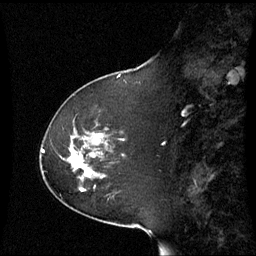
Breast MRI (dynamic contrast-enhanced), one sagittal slice; dynamic contrast-enhanced series, image 2 of 3 at this slice position (ordered by acquisition); 1.5 T; TE 4.2 ms, TR 8.9 ms; 2.4 mm slice thickness; 256 × 256 image matrix, field of view 230 × 230 mm. Female patient, age 51 years. From the clinical record (not read from this slice): setting: breast cancer imaged before/during neoadjuvant chemotherapy; receptor status: HR-positive, HER2-negative.
Annotated regions visible in this slice (semi-automatically segmented with operator editing):
- analysis volume of interest (the breast-tissue region the enhancement analysis was run in; not a lesion): bounding box <42,123,110,192> (left, top, right, bottom; pixels)
- tumour enhancement mask (voxels above the 70 % enhancement threshold inside the analysis volume of interest): <68,153,85,168>